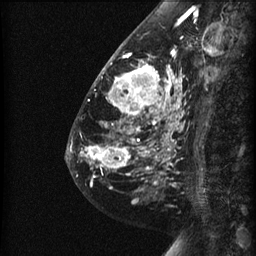
Breast MRI (dynamic contrast-enhanced), one sagittal slice; position 22 of 60 along the scan axis; dynamic contrast-enhanced series, image 2 of 3 at this slice position (ordered by acquisition); 1.5 T; TE 4.2 ms, TR 22.7 ms; 1.5 mm slice thickness; 256 × 256 image matrix, field of view 180 × 180 mm. Female patient, age 48 years. Case-level facts recorded for this patient, not image findings: setting: breast cancer imaged before/during neoadjuvant chemotherapy; receptor status: triple-negative.
Annotated regions visible in this slice (semi-automatically segmented with operator editing):
- analysis volume of interest (the breast-tissue region the enhancement analysis was run in; not a lesion): bounding box <89,27,191,180> (left, top, right, bottom; pixels)
- tumour enhancement mask (voxels above the 90 % enhancement threshold inside the analysis volume of interest): <89,54,182,176>